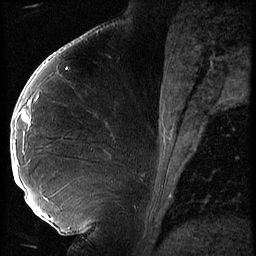
Breast MRI (dynamic contrast-enhanced), one sagittal slice; slice 27 of 56 in the series (ordered by position); 3 images stored at this slice position (order not interpretable as contrast timing); 1.5 T; TE 4.2 ms, TR 9 ms; 2.5 mm slice thickness; 256 × 256 image matrix. Female patient, age 43 years. From the clinical record (not read from this slice): setting: breast cancer imaged before/during neoadjuvant chemotherapy; receptor status: HER2-positive.
Structures marked on this image (semi-automatic segmentation, software-assisted and operator-edited):
- analysis volume of interest (the breast-tissue region the enhancement analysis was run in; not a lesion): bounding box <11,92,74,211> (left, top, right, bottom; pixels)
- tumour enhancement mask (voxels above the 140 % enhancement threshold inside the analysis volume of interest): <14,141,16,143>